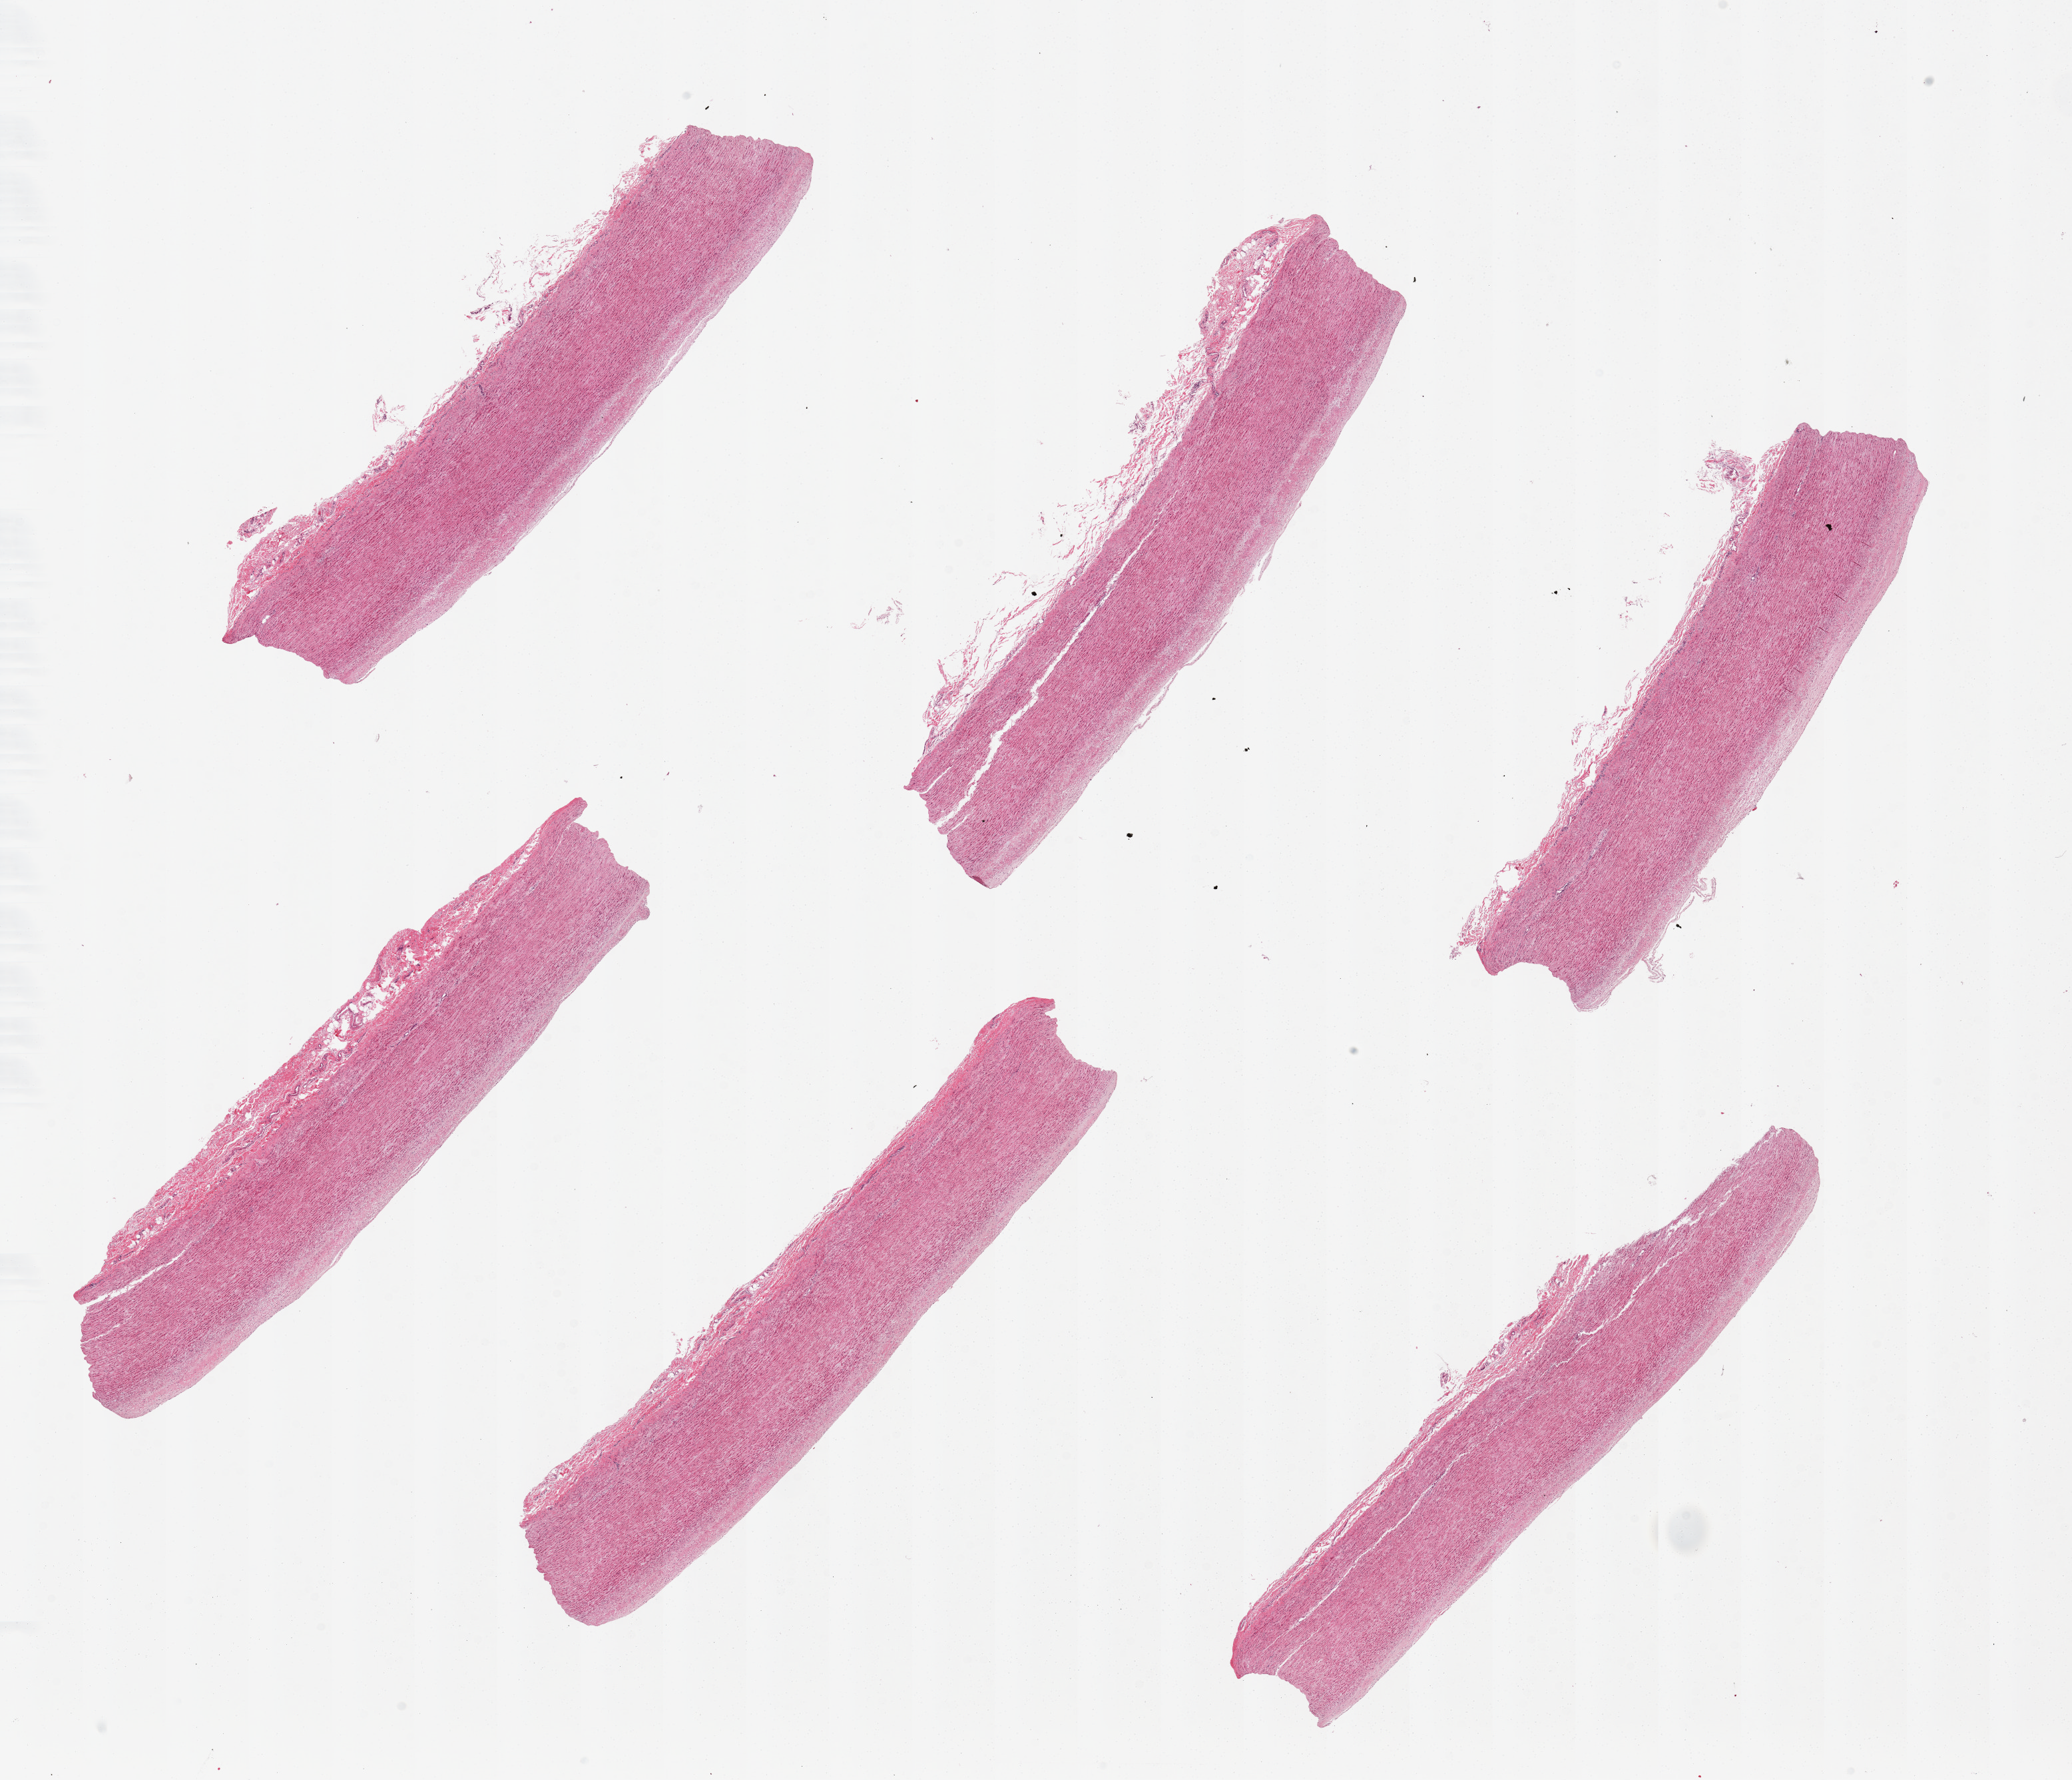
H&E whole-slide image, brightfield, low-resolution overview of the scanned area, about 24.6 x 21.1 mm (acquisition: 20x scan); PAXgene-fixed paraffin-embedded (PFPE) section; section of aorta (target tissue); tissue donor sample. Donor: male.
Review note (as recorded): 6 pieces; some intimal thickening.